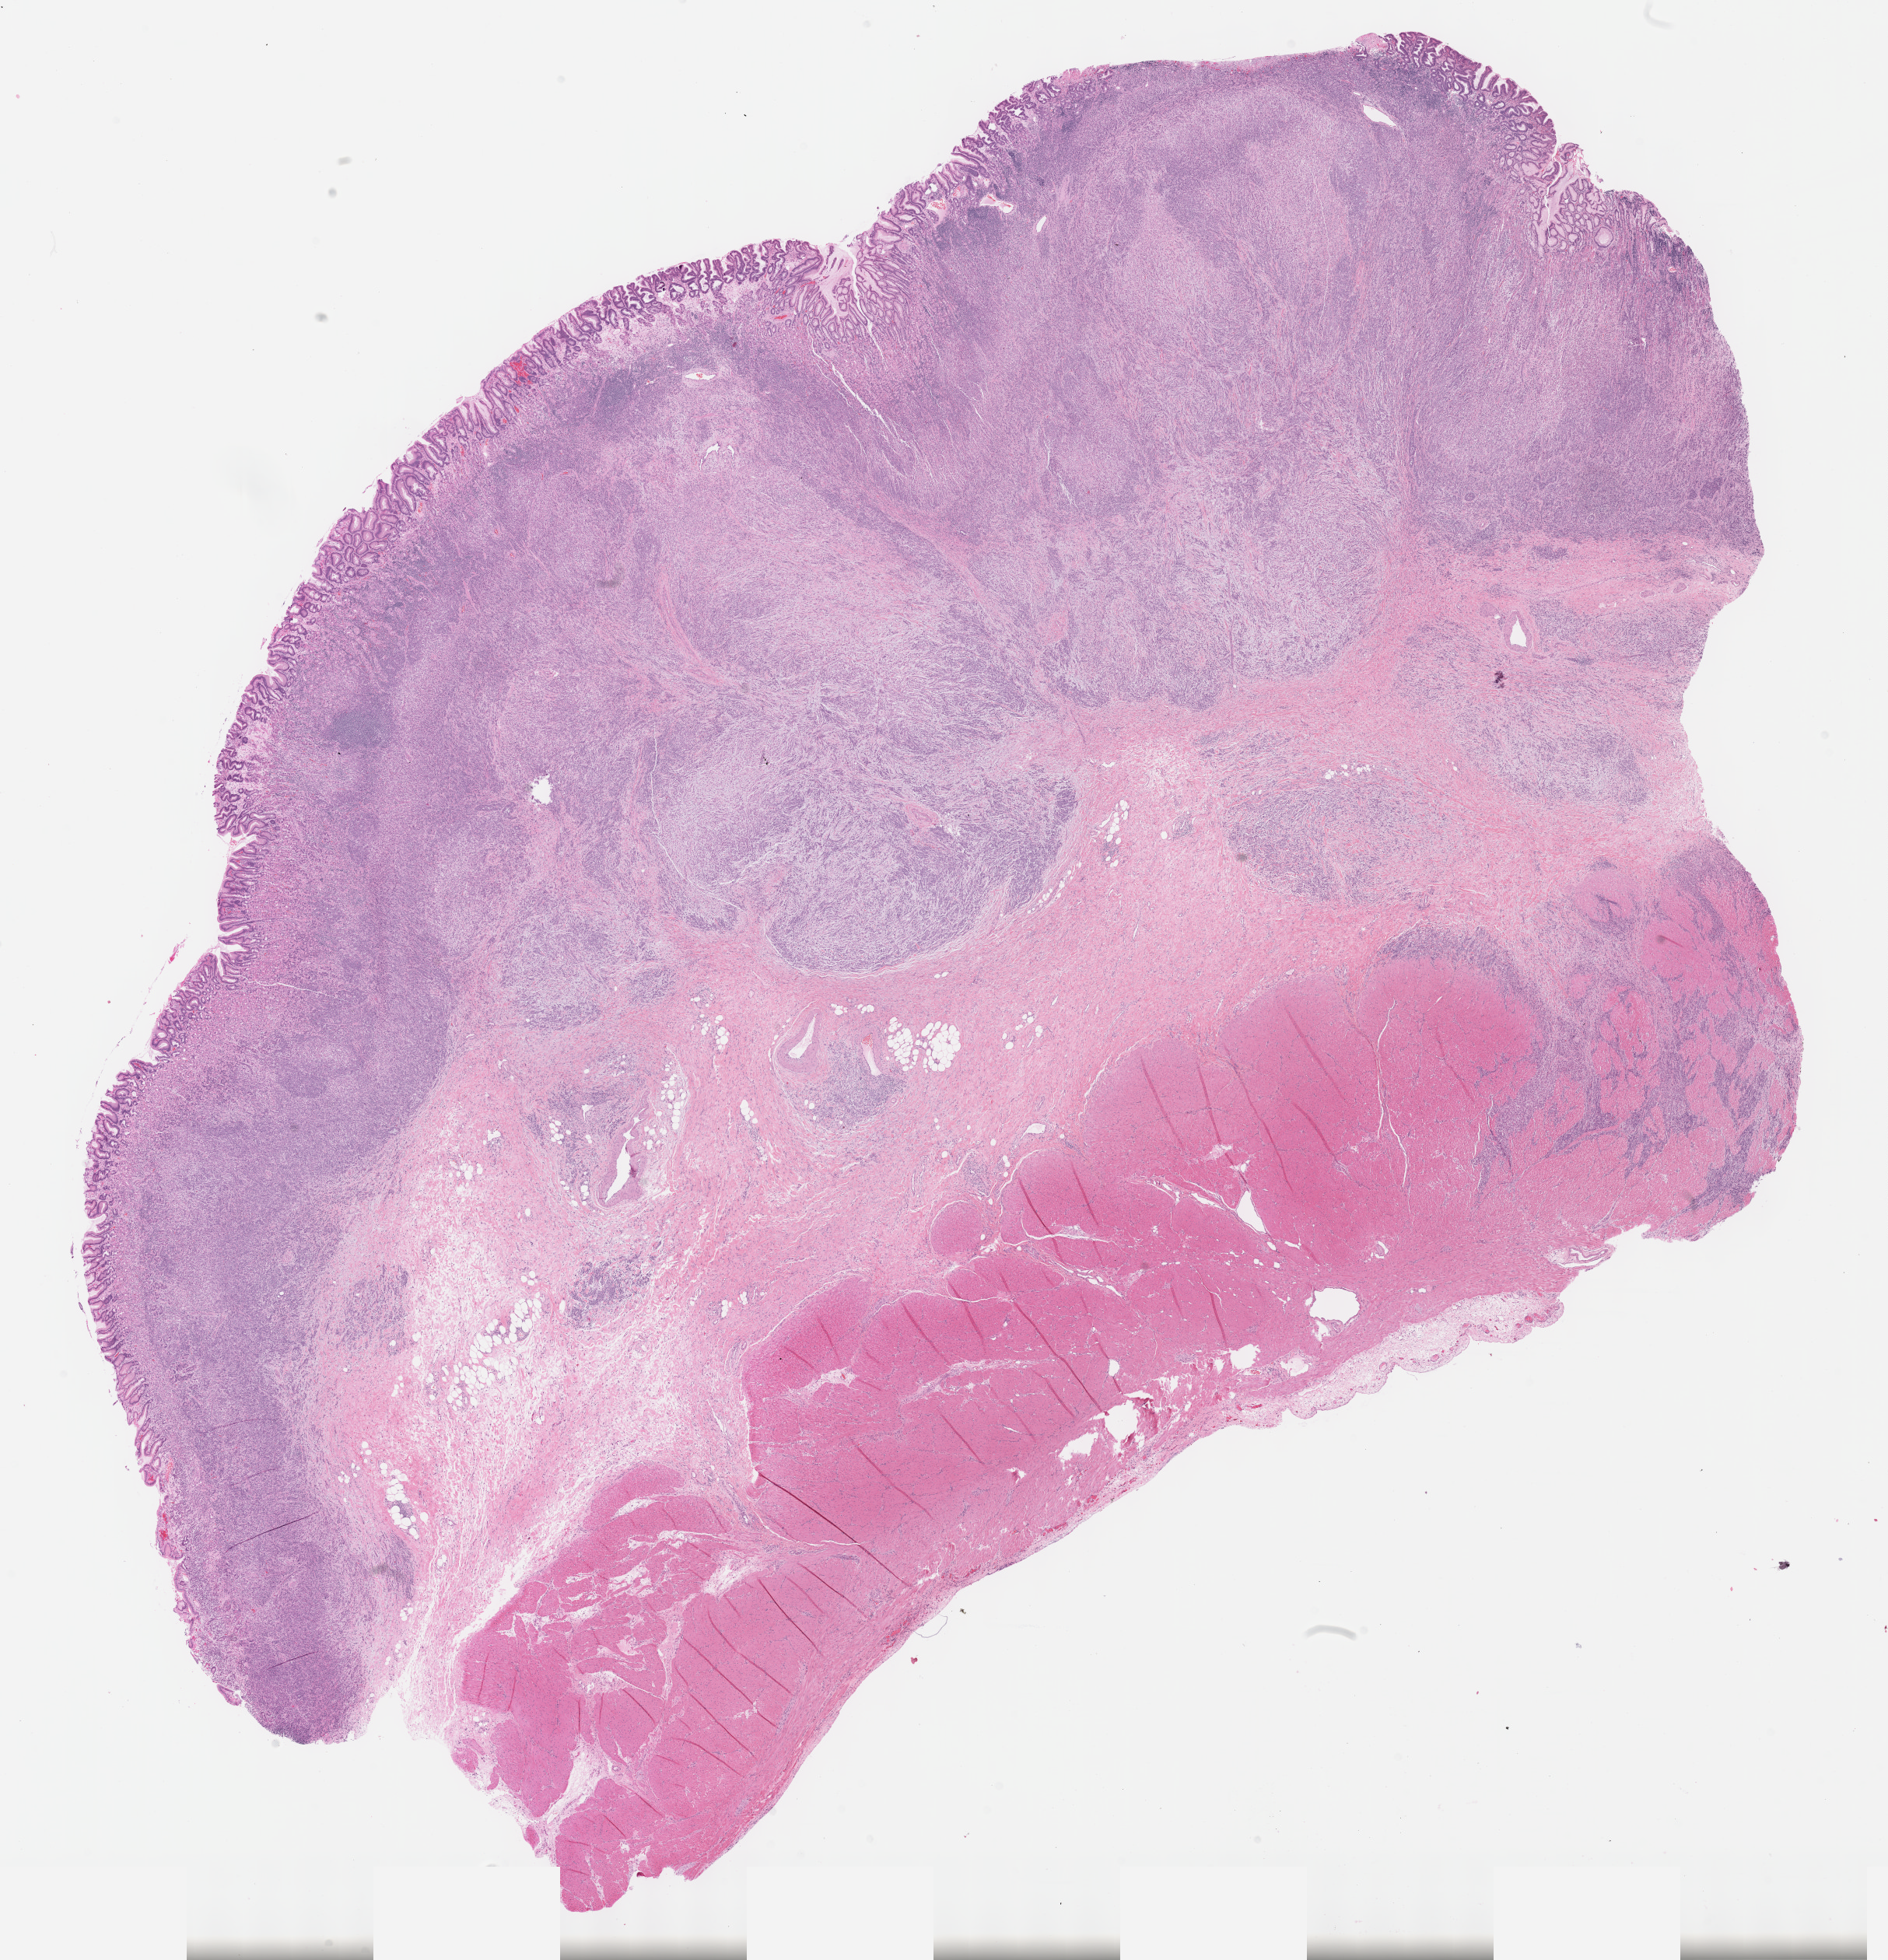
Digitized H&E-stained tissue section (whole slide) — whole scanned area (about 19.6 x 20.4 mm, slide scanned at 40x) shown as a low-resolution overview; formalin-fixed paraffin-embedded (FFPE) diagnostic section; stomach, primary tumour sample. Male, age 51 years at initial diagnosis. Histologic grade: G3 (poorly differentiated).
• TNM: T3 N2 MX
• AJCC pathologic stage: IIIB (6th edition)
• diagnosis: Adenocarcinoma, NOS